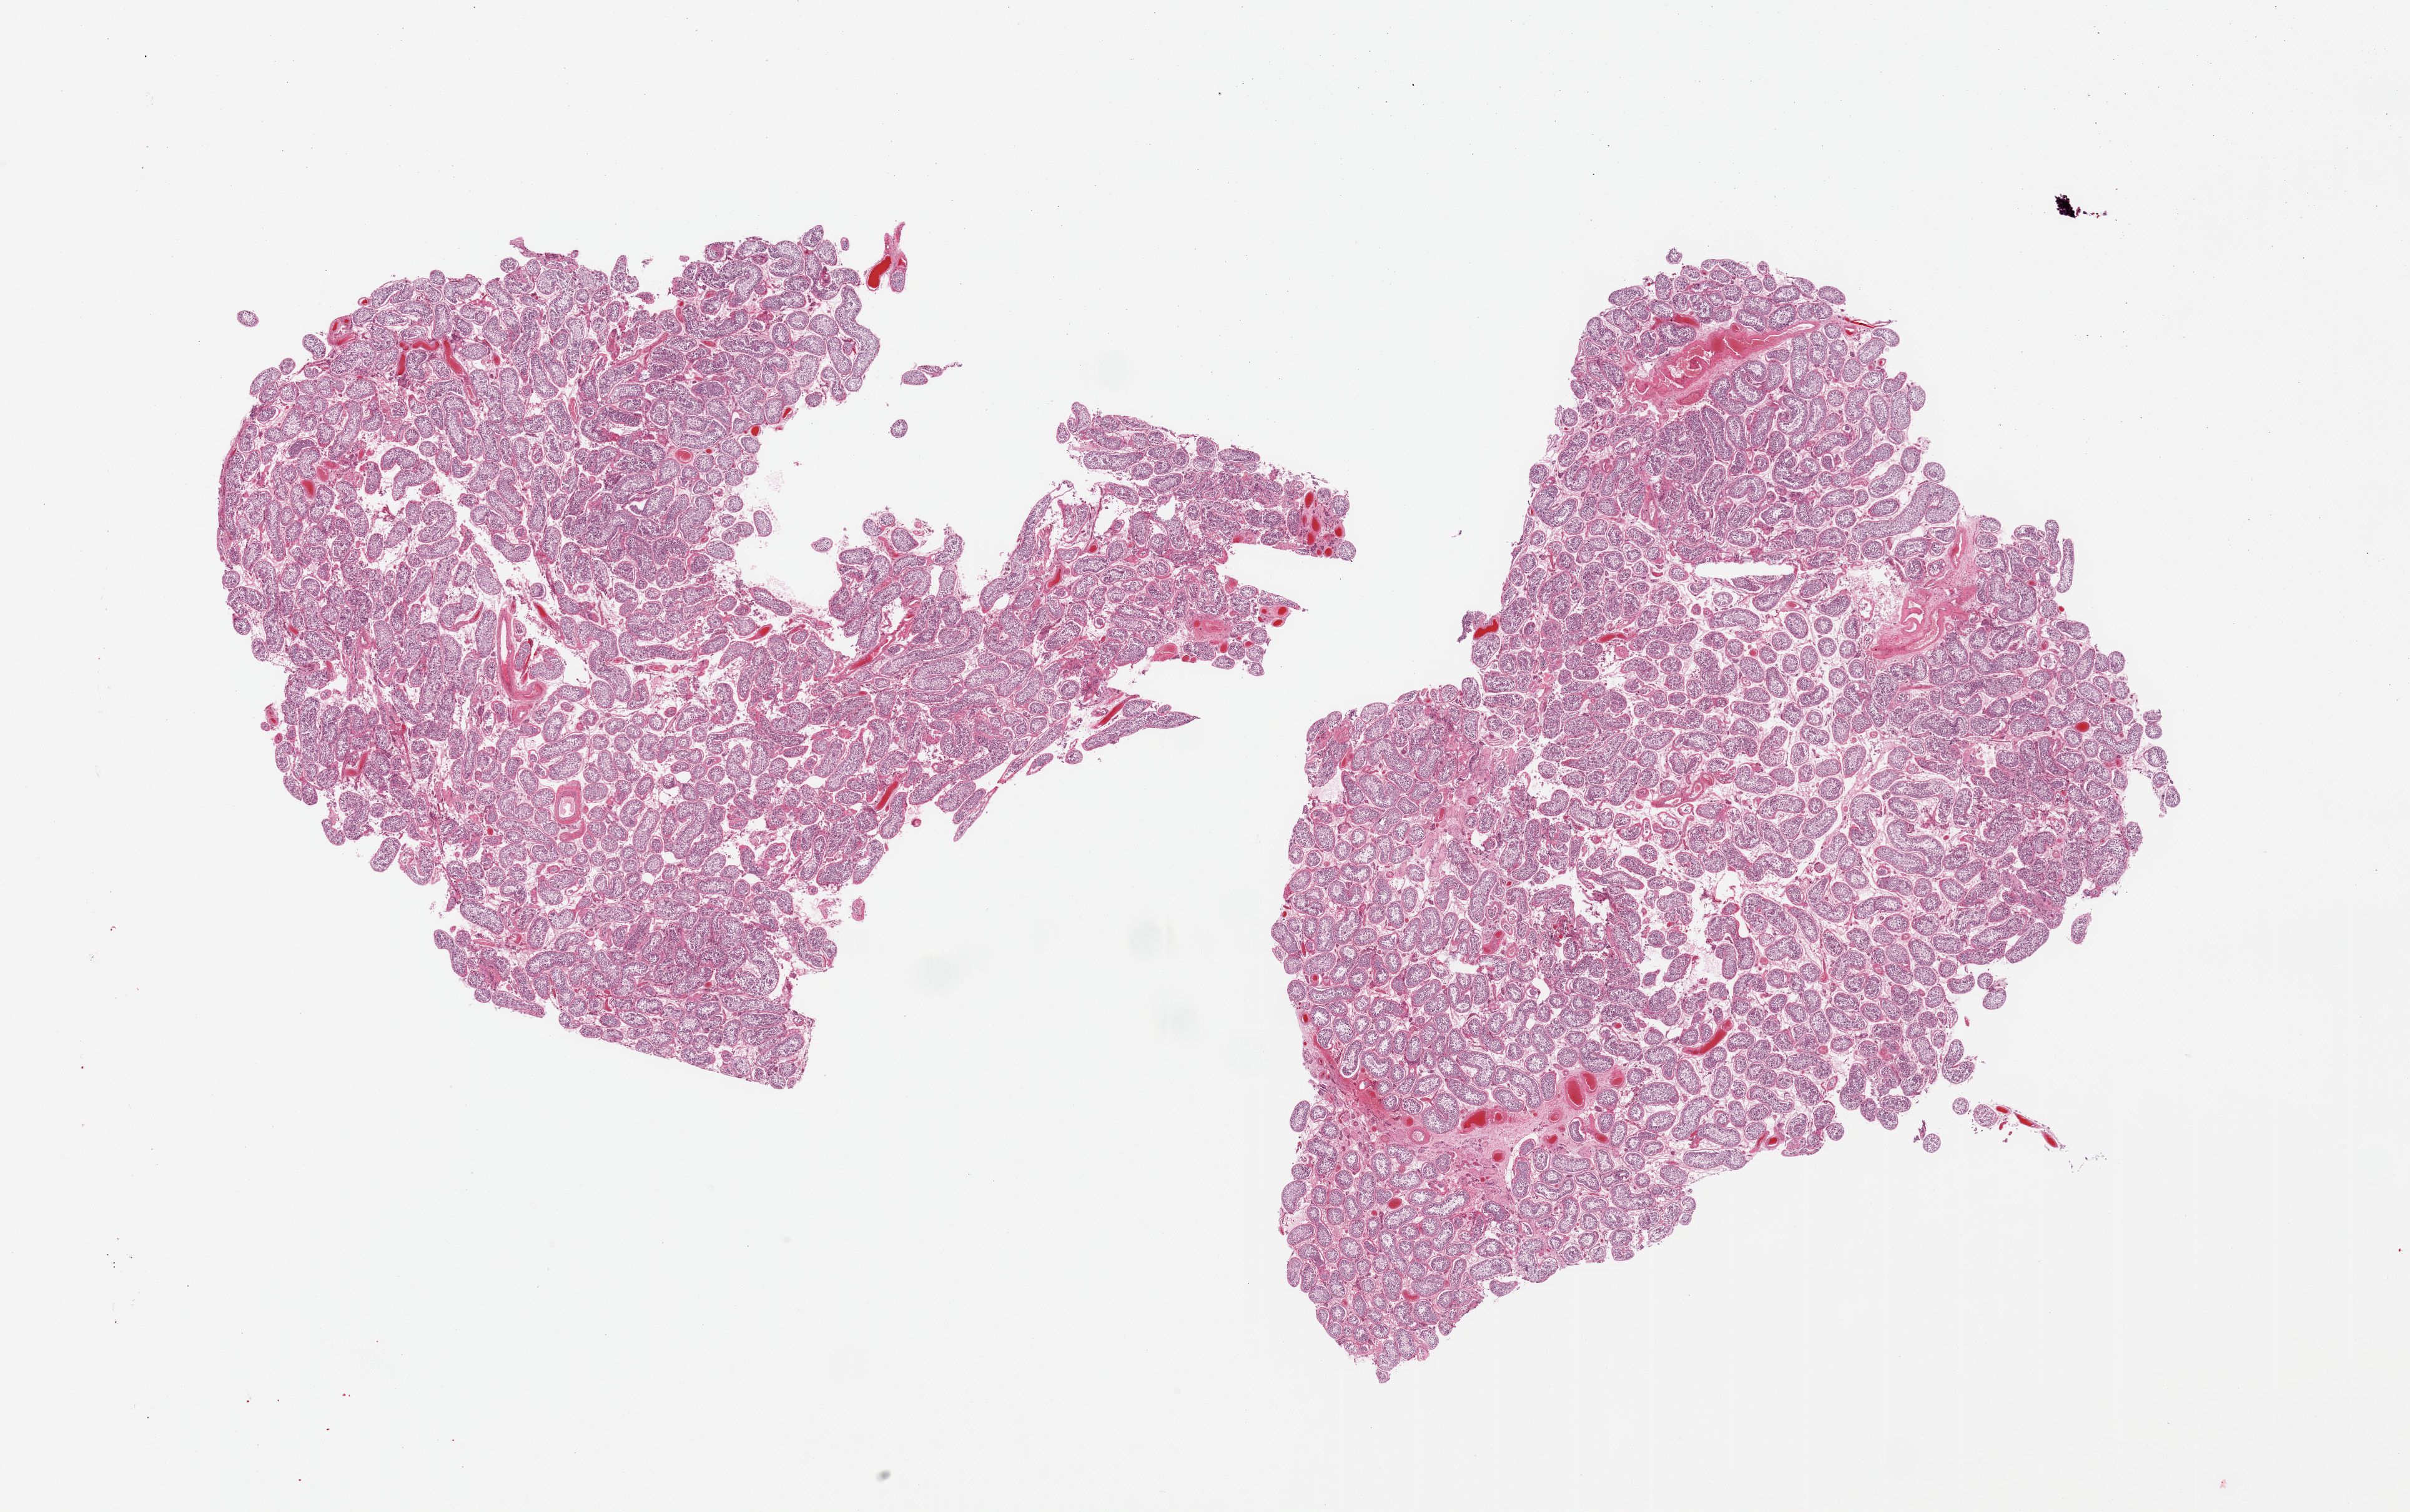
Whole-slide image, H&E stain, brightfield, low-resolution overview of the scanned area, about 30.5 x 19.1 mm (acquisition: 20x scan), PAXgene-fixed paraffin-embedded (PFPE) section, sampled site (target tissue): testis, tissue donor sample.
Reviewer comment on this tissue sample: 2 pieces; active spermatogenesis.